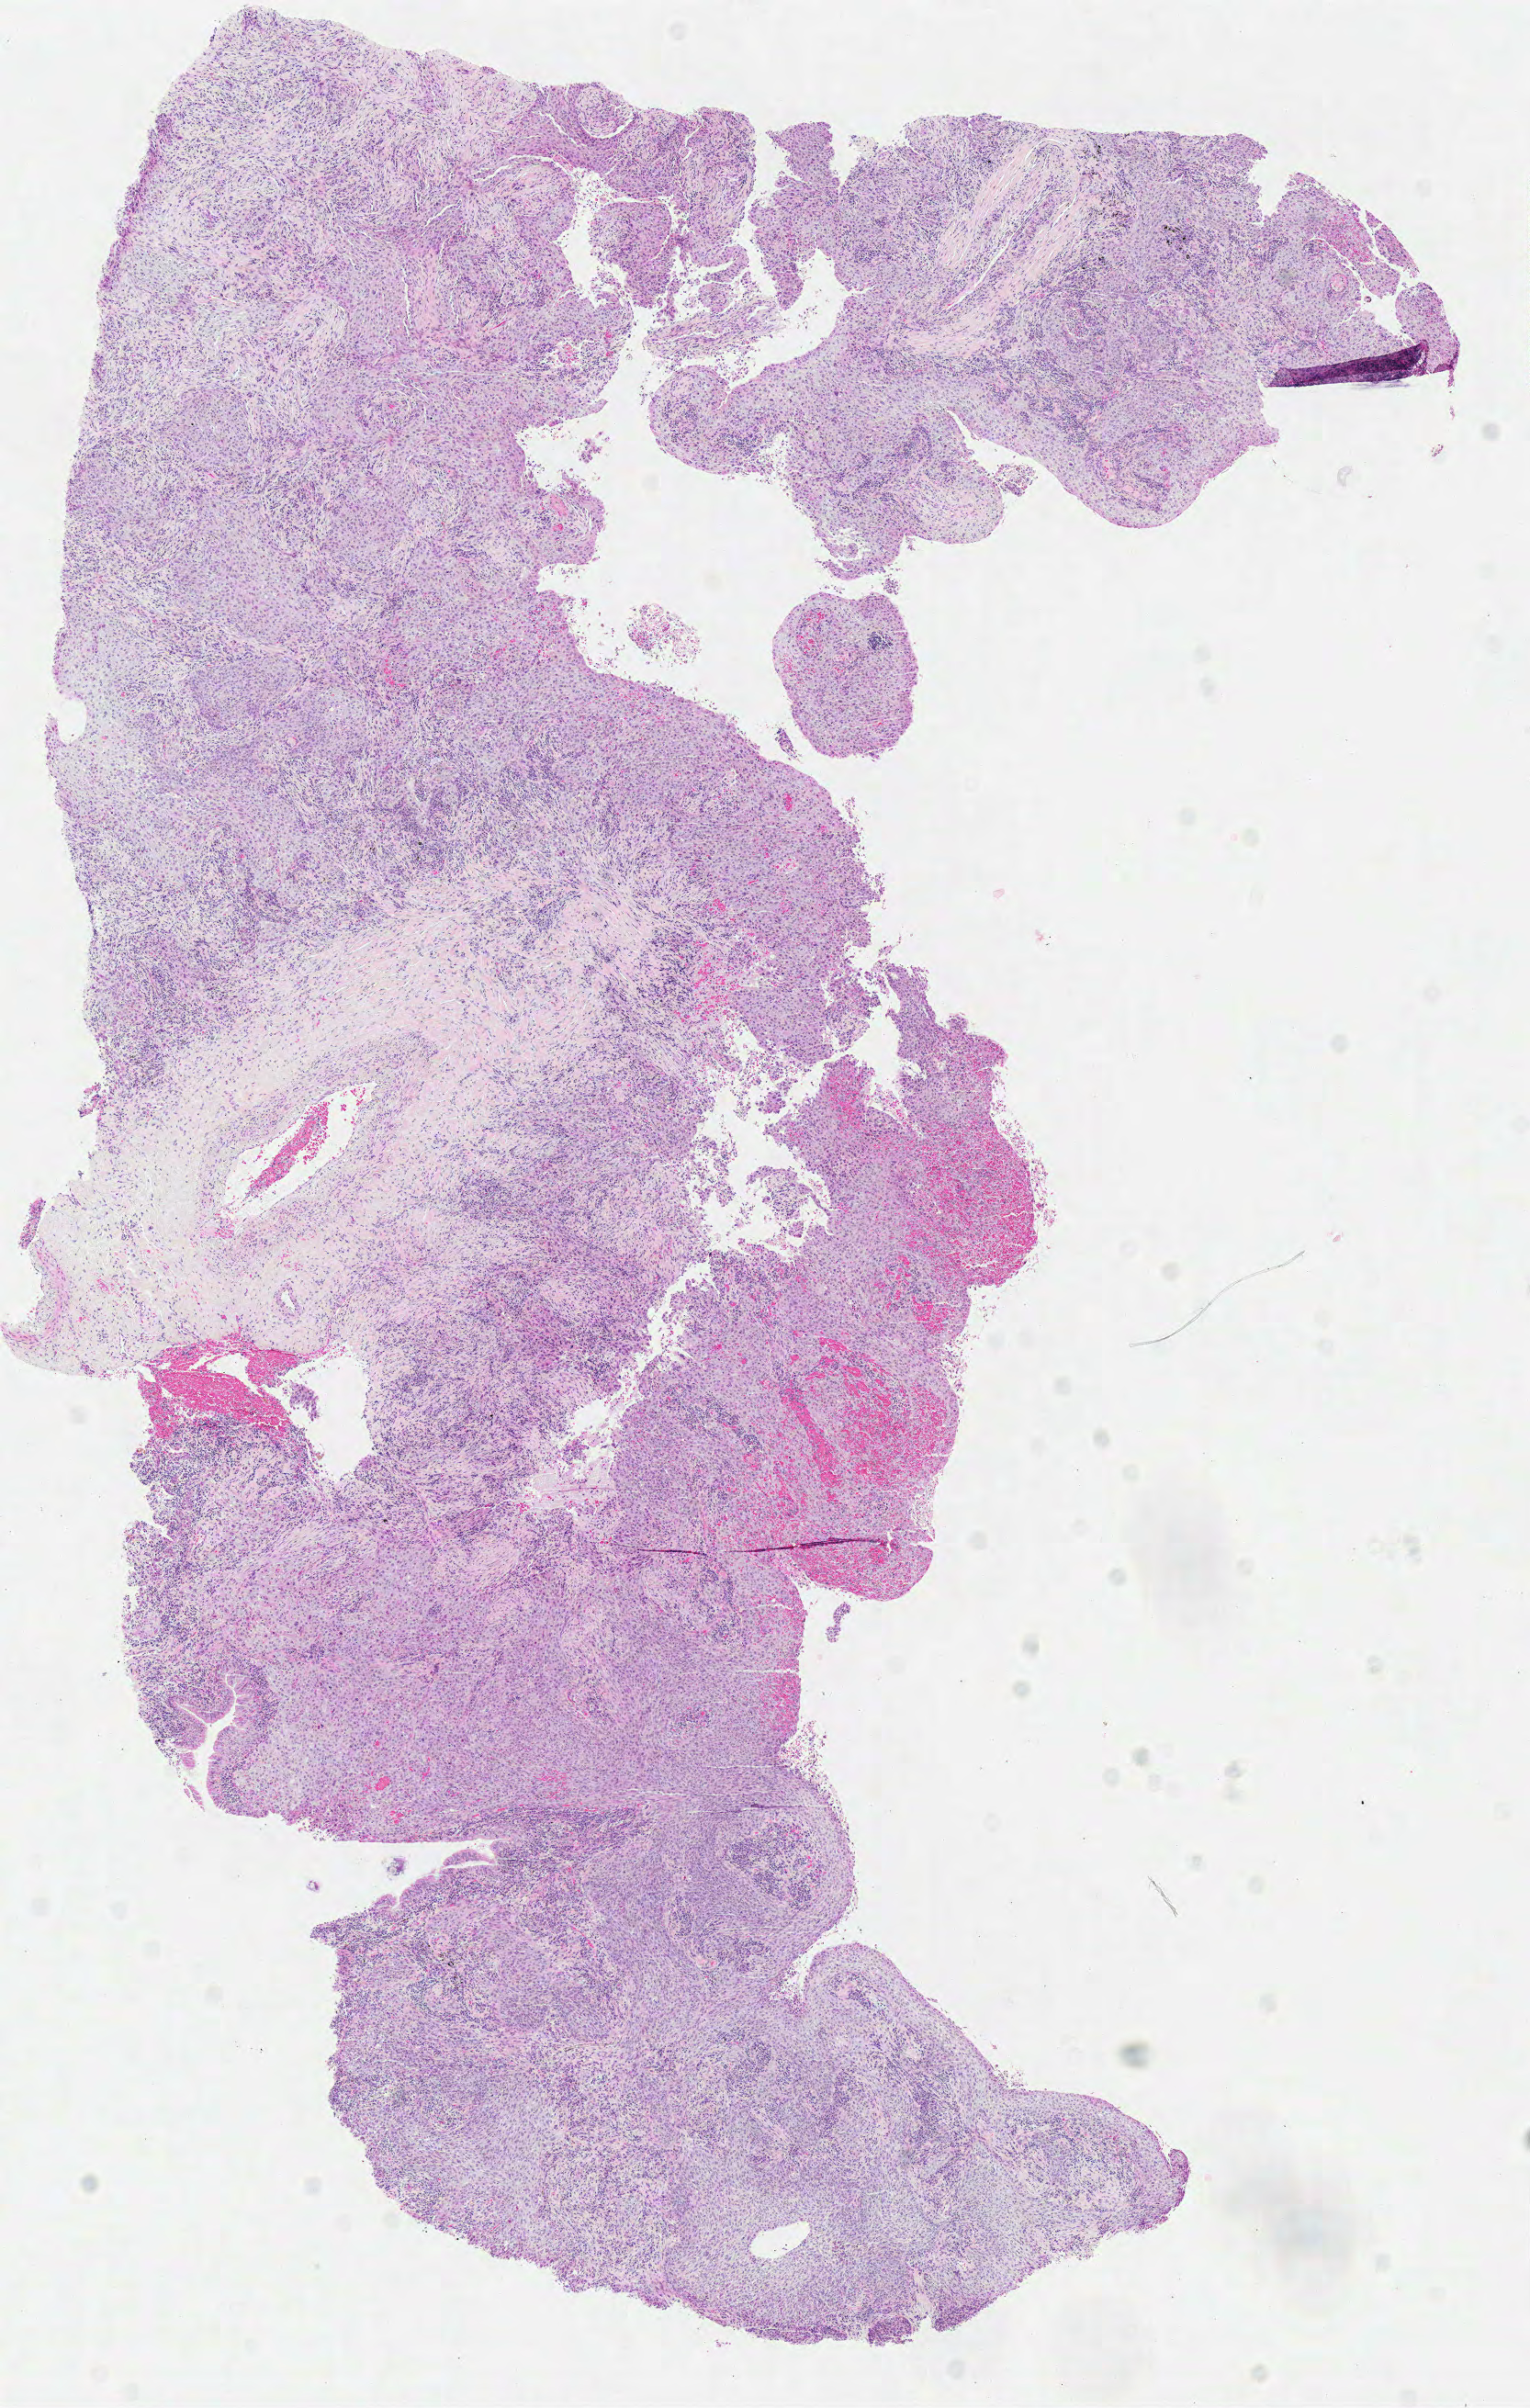
Whole-slide histology image, H&E, whole scanned area (about 6.6 x 10.3 mm, slide scanned at 40x) shown as a low-resolution overview; formalin-fixed paraffin-embedded (FFPE) diagnostic section; primary tumour sample from the lung. Patient: male, age at initial diagnosis 64 years.
TNM: T2 N0 M0. AJCC pathologic stage: IB. Diagnosis: Squamous cell carcinoma, NOS (lower lobe, lung).